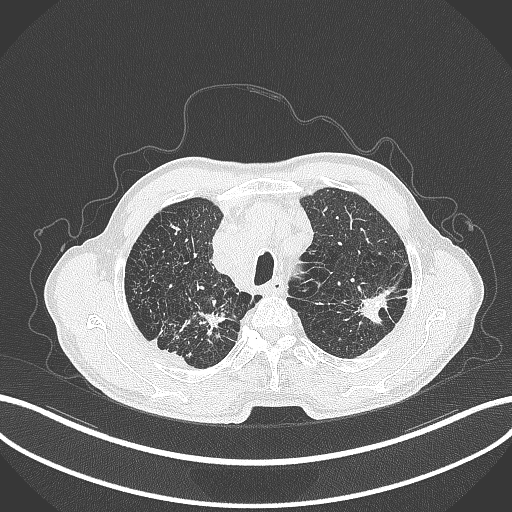
Chest CT, one axial slice. Slice 367 of 463 in the series (ordered by position). Reconstruction kernel B70f. 120 kVp. Lung window (W 1500 / L -600 HU). 512 × 512 image matrix. Patient: male, 74 years. From the clinical record (not read from this slice): clinical TNM (as recorded): T2a N1 M0.
Annotated regions visible in this slice (rectangle marked by the reading radiologist):
- lung tumour (recorded histology: adenocarcinoma): bounding box [x1, y1, x2, y2] px = [355, 286, 397, 331]